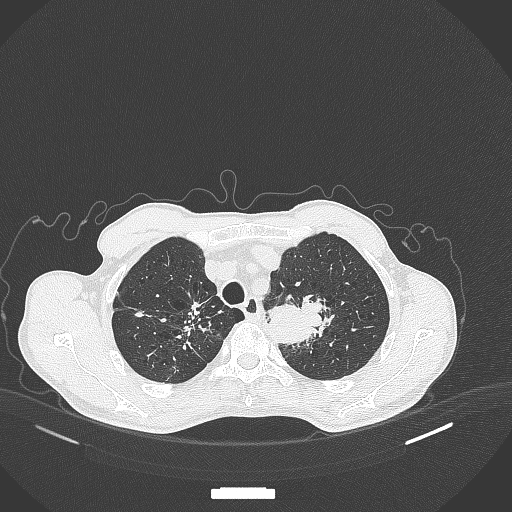
Chest CT, one axial slice; position 353 of 386 along the scan axis; reconstruction kernel B70f; lung window (W 1500 / L -600 HU); 1 mm slice thickness; 512 × 512 image matrix, field of view 400 × 400 mm. Patient: male, 65 years. From the clinical record (not read from this slice): clinical TNM (as recorded): T2b N0 M0; histopathological grade: G2.
Structures marked on this image (bounding box drawn by a radiologist):
- lung tumour (recorded histology: adenocarcinoma): bounding box [x1, y1, x2, y2] px = [268, 293, 335, 350]